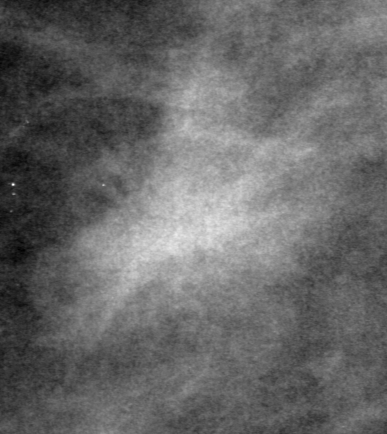
Region of interest cut from a scanned film mammogram (one marked finding); left breast; CC view.
Finding: mass, shape irregular, margins spiculated; BI-RADS assessment category 3; subtlety rating 2 on a 1 (subtle) to 5 (obvious) scale; pathology result (as recorded, not read from the image): malignant.